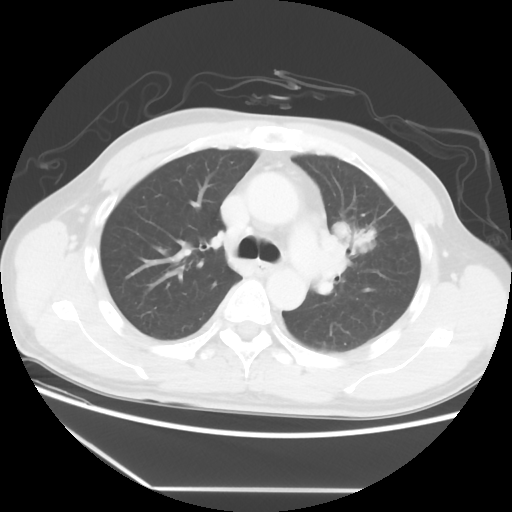
Chest CT, one axial slice; position 37 of 56 along the scan axis; 120 kVp; lung window (W 1500 / L -600 HU); 512 × 512 image matrix, field of view 373 × 373 mm. Male patient, age 53 years. From the clinical record (not read from this slice): clinical TNM (as recorded): T2a N1 M1b.
Structures marked on this image (rectangle marked by the reading radiologist):
- lung tumour (recorded histology: adenocarcinoma): bounding box (x1, y1, x2, y2) in pixels: (336, 223, 375, 254)